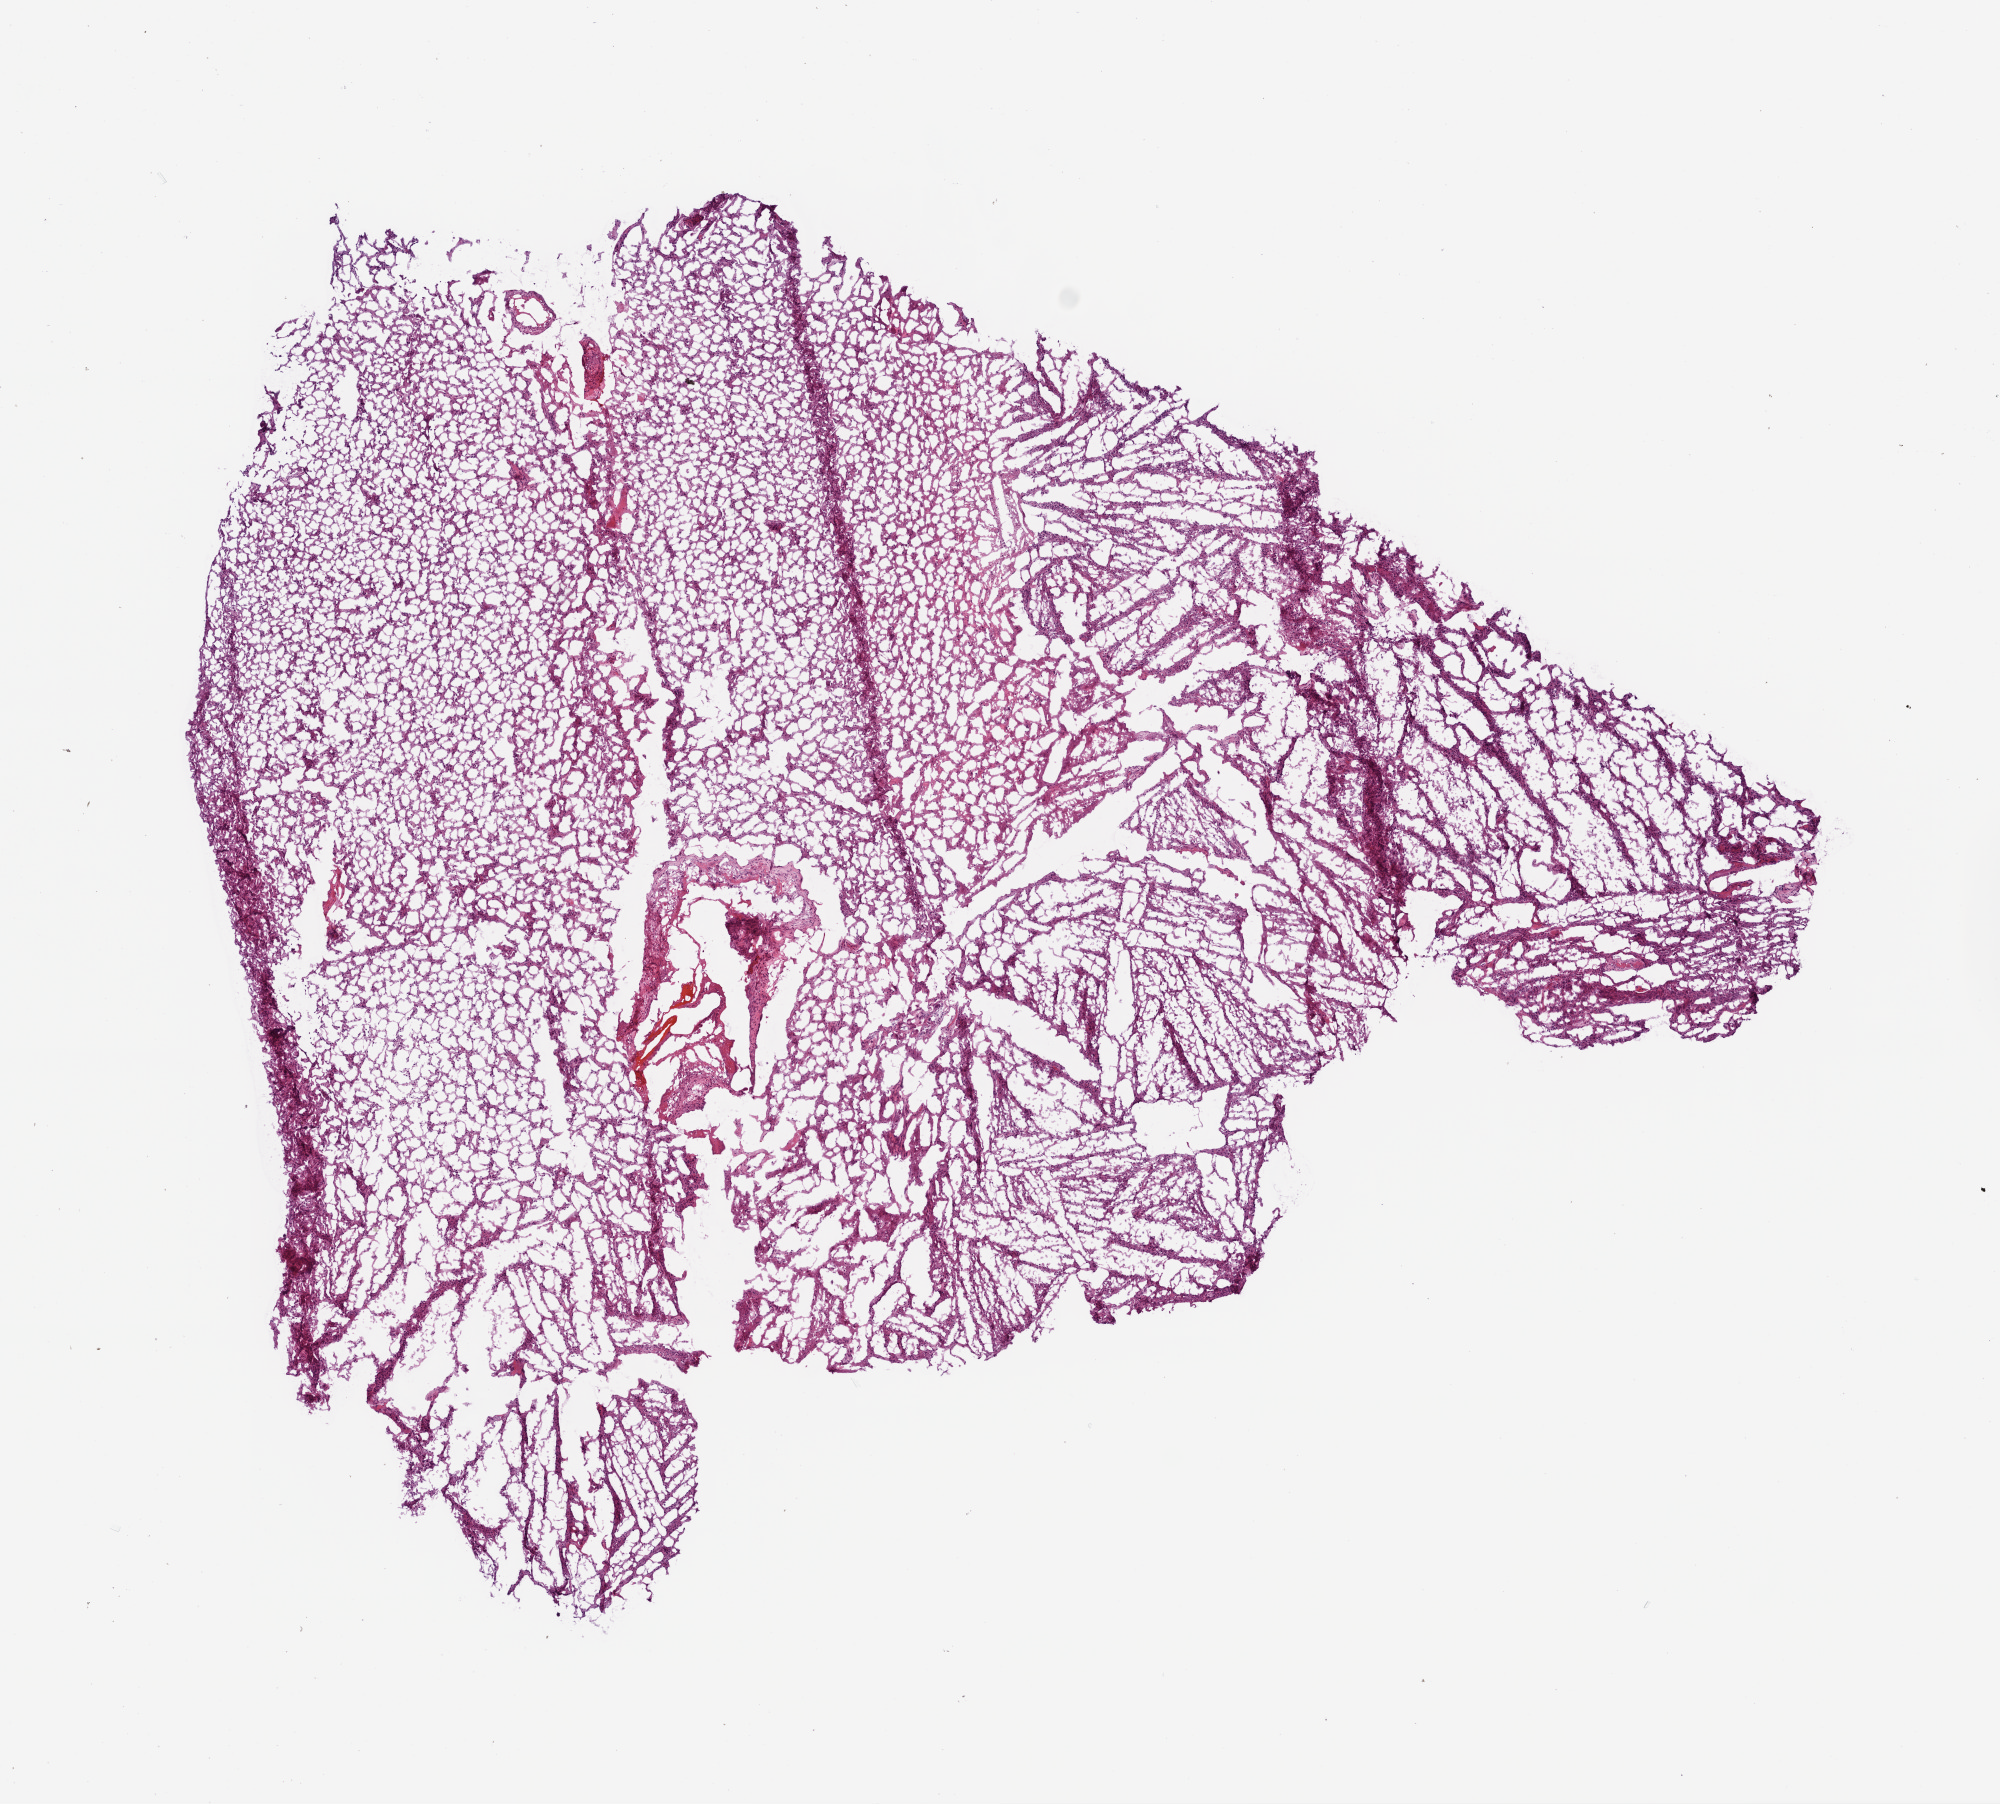
H&E-stained whole-slide image — low-resolution overview of the scanned area, about 8.0 x 7.2 mm; frozen section from the bottom of the tissue portion; primary tumour sample from the brain. Female, age 65 years at initial diagnosis. Slide review estimates, as recorded: tumour cells 100%, tumour nuclei 75%, normal cells 0%, stromal cells 0%, necrosis 0%.
Histologic diagnosis: Glioblastoma.